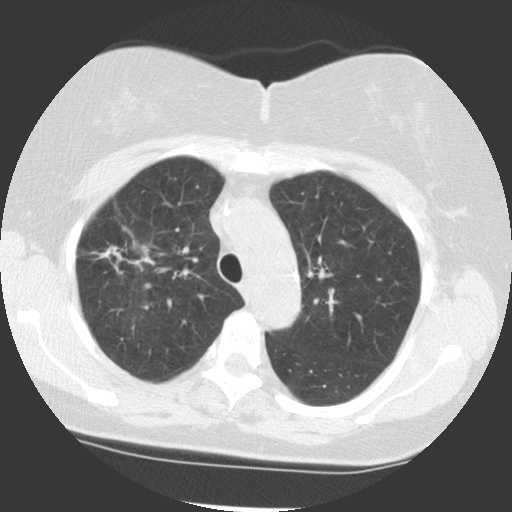
Low-dose screening chest CT, axial slice, baseline annual screen, lung window (W 1500 / L -600 HU), 2.5 mm slice thickness, 140 kVp, slice 86 of 113 in the series. Female, age 68 years at enrolment.
• Expert reader's lesion annotation, bounding box [x1, y1, x2, y2] px = [86, 227, 157, 286].
• Reader record for this screening exam (exam-level; its link to the box is not recorded): non-calcified nodule or mass ≥4 mm, right upper lobe, 42 × 20 mm, spiculated (stellate) margins, soft tissue attenuation.
• Participant outcome: lung cancer diagnosed 51 days after this screen — adenocarcinoma, NOS, right upper lobe, moderately differentiated (G2), stage IB (AJCC 6th edition), 31 mm at pathology.